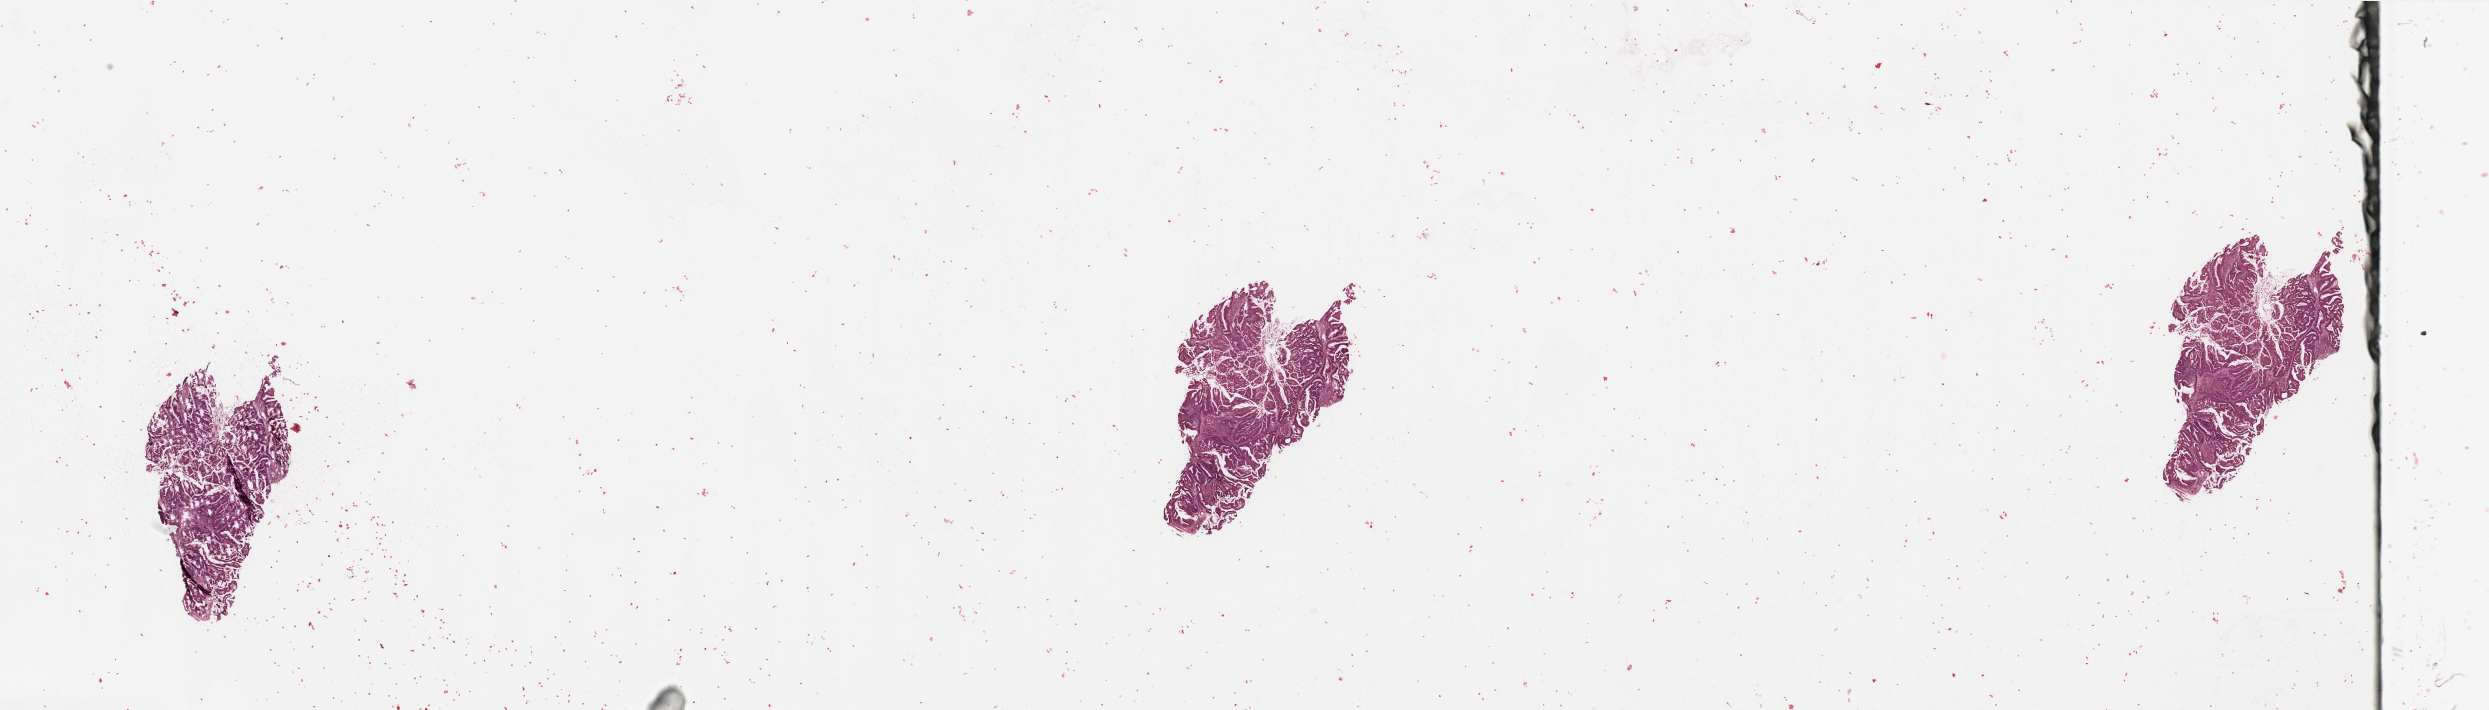
Whole-slide histology image, H&E-stained, whole scanned area (about 39.4 x 11.2 mm, acquisition: 20x scan) shown as a low-resolution overview. Tumour tissue sample, sampled site: uterus. Patient: female, age 64 years. Slide review estimates, as recorded: tumour nuclei 80%, necrosis 2%.
Histologic diagnosis: Endometrioid adenocarcinoma, NOS.